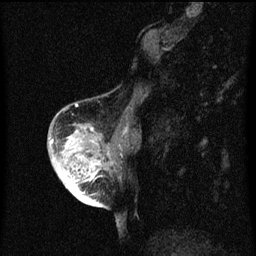
Breast MRI (dynamic contrast-enhanced), one sagittal slice; position 22 of 60 along the scan axis; dynamic contrast-enhanced series, image 2 of 3 at this slice position (ordered by acquisition); 1.5 T; TE 4.2 ms, TR 8 ms; 2 mm slice thickness; 256 × 256 image matrix, field of view 180 × 180 mm. Female patient, age 56 years.
Outlined on this slice (semi-automatic segmentation, software-assisted and operator-edited):
- analysis volume of interest (the breast-tissue region the enhancement analysis was run in; not a lesion): box from (x=54, y=122) to (x=116, y=199) px
- tumour enhancement mask (voxels above the 70 % enhancement threshold inside the analysis volume of interest): (x=63, y=132)–(x=101, y=199)